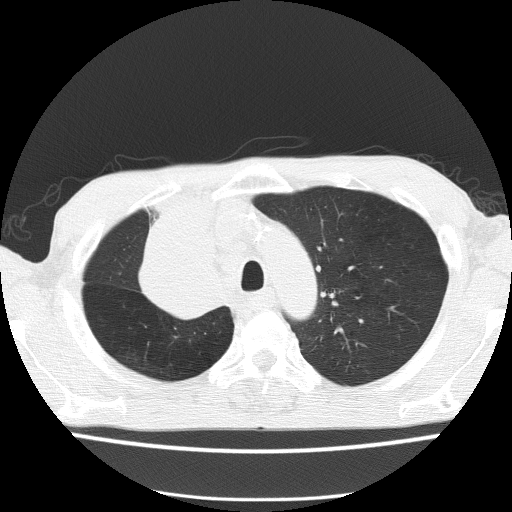
Axial slice from a low-dose chest CT screening exam, baseline annual screen, lung window (W 1500 / L -600 HU), 2 mm slice thickness. Male, age 59 years at enrolment.
- Expert-annotated lung lesion, bounding box [x1, y1, x2, y2] px = [131, 234, 239, 326].
- The screening reader recorded 5 non-calcified nodules or masses ≥4 mm on this exam; which of them this box marks is not recorded.
- Official screen result: positive, change unspecified: nodule(s) >= 4 mm or enlarging nodule(s), mass(es), or other non-specific abnormalities suspicious for lung cancer.
- Lung cancer was diagnosed 72 days after this screen: squamous cell carcinoma, NOS, right upper lobe, moderately differentiated (G2), stage IV (AJCC 6th edition).